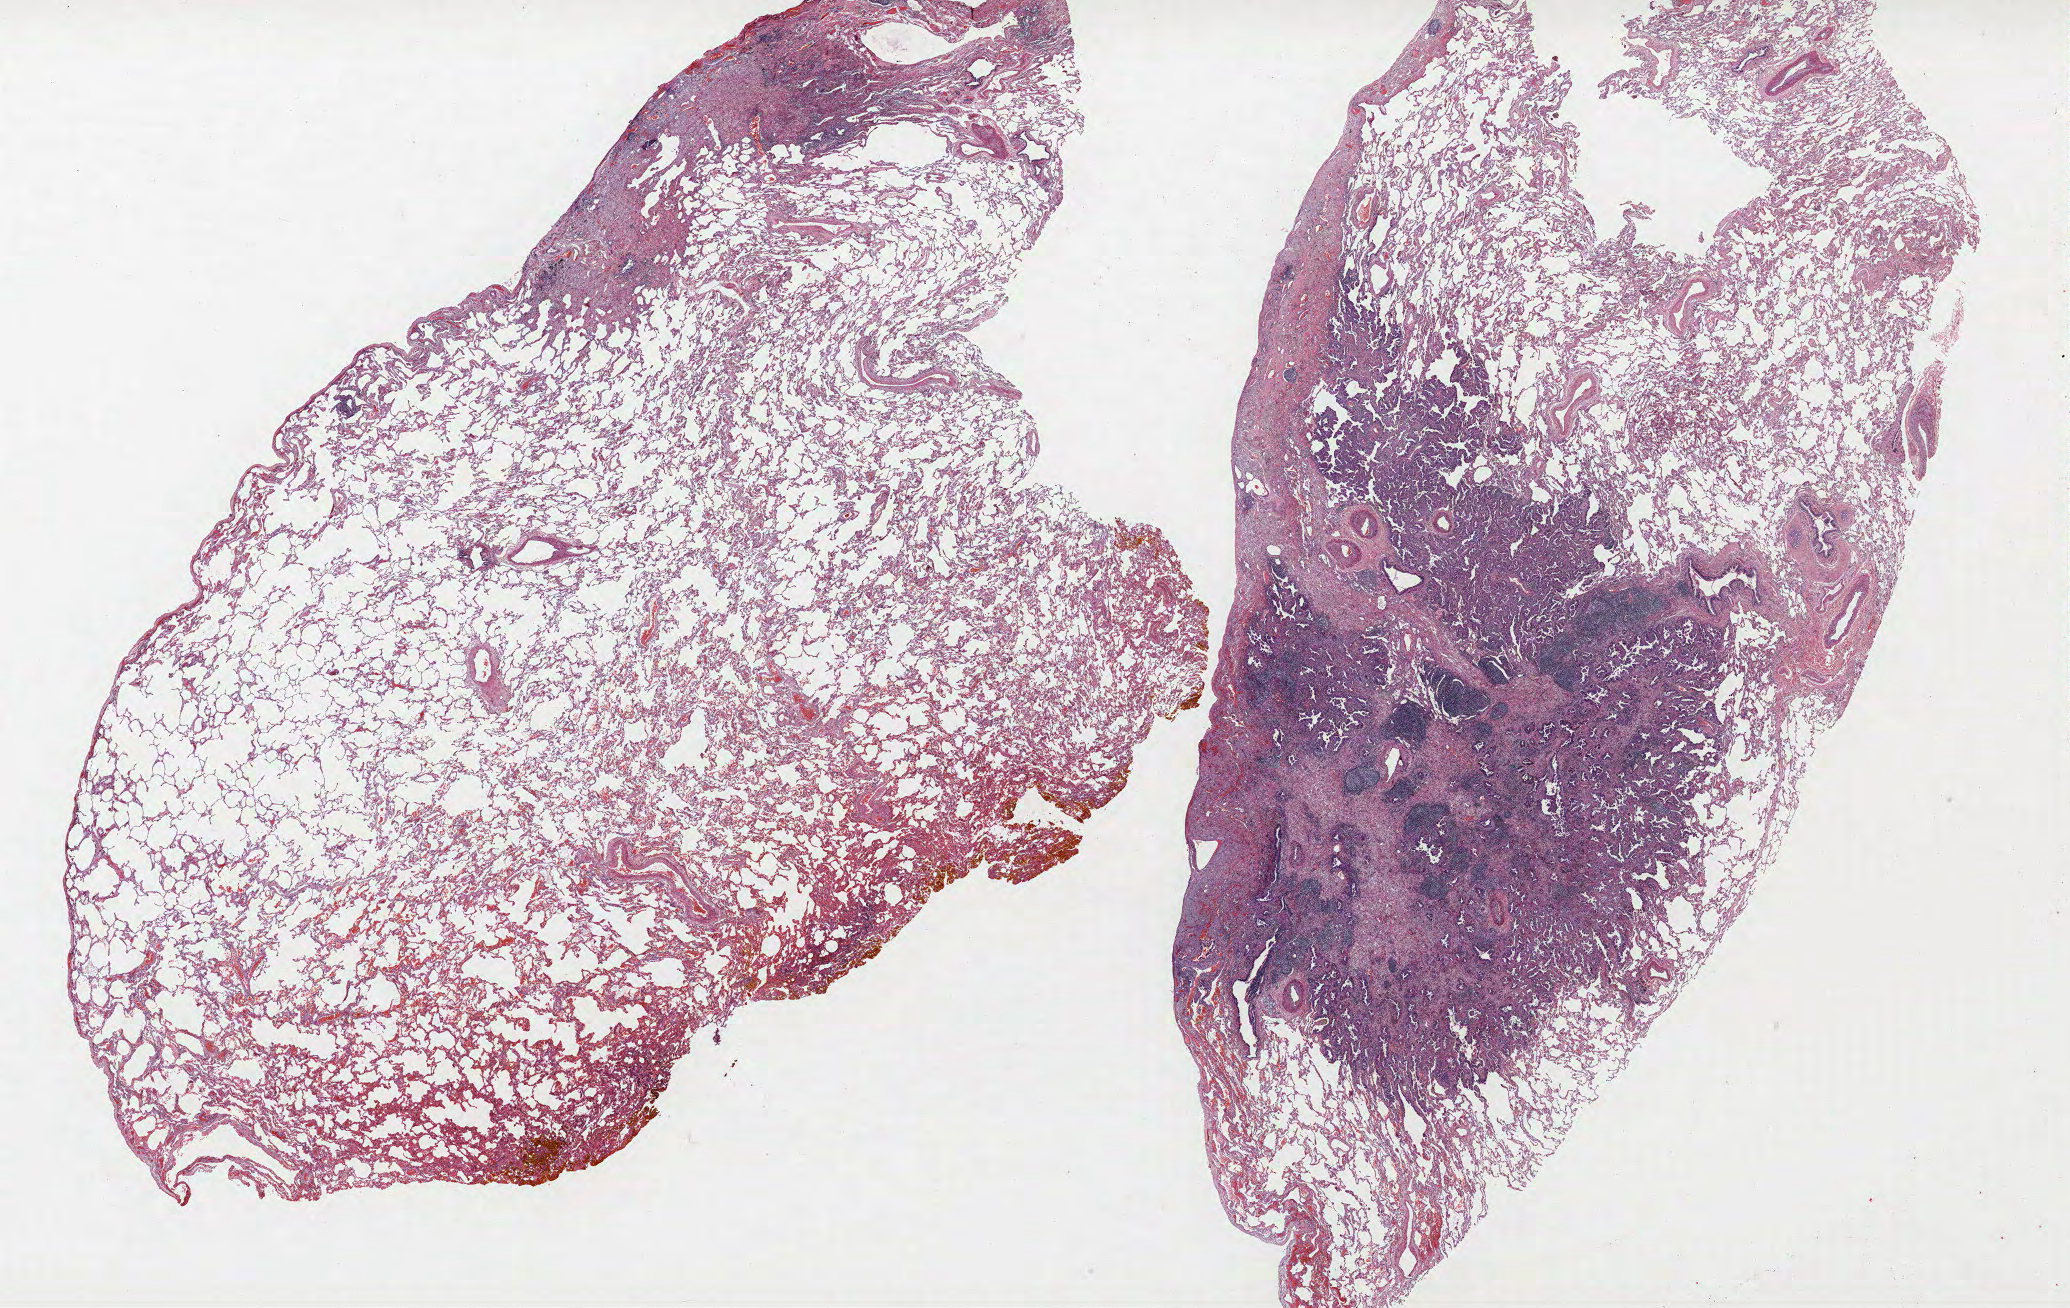
H&E whole-slide image — low-resolution overview of the scanned area, about 33.1 x 20.9 mm; formalin-fixed paraffin-embedded (FFPE) section; lung. Male, age 56 at enrolment. Former smoker at enrolment. Grade: moderately differentiated (G2).
Participant's lung-cancer diagnosis: Adenocarcinoma, NOS (ICD-O-3 8140/3). Tumour size (pathology): 9 mm. ICD-O-3 topography: upper lobe of lung (C34.1). Primary tumour location (clinical record): right upper lobe. Stage (AJCC 6th edition): IA.